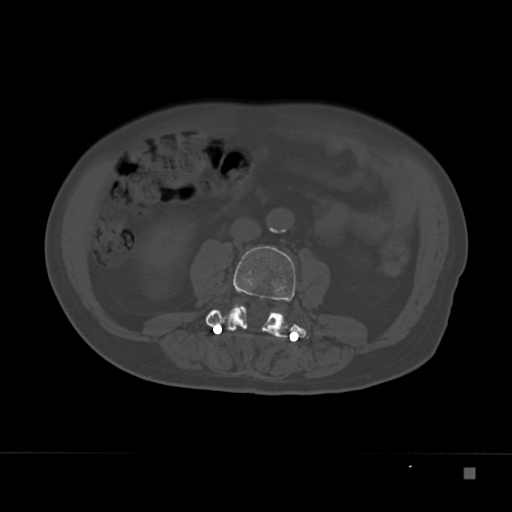
CT including the spine, one axial slice; position 64 of 332 along the scan axis; bone window (W 1800 / L 400 HU); 1.5 mm slice thickness; 512 × 512 image matrix, field of view 389 × 389 mm. Patient: male, 72 years. From the clinical record (not read from this slice): primary cancer: skeletal.
Outlined on this slice (semi-automatically segmented with operator editing):
- L3 vertebra: bounding box (x1, y1, x2, y2) in pixels: (206, 246, 309, 342)